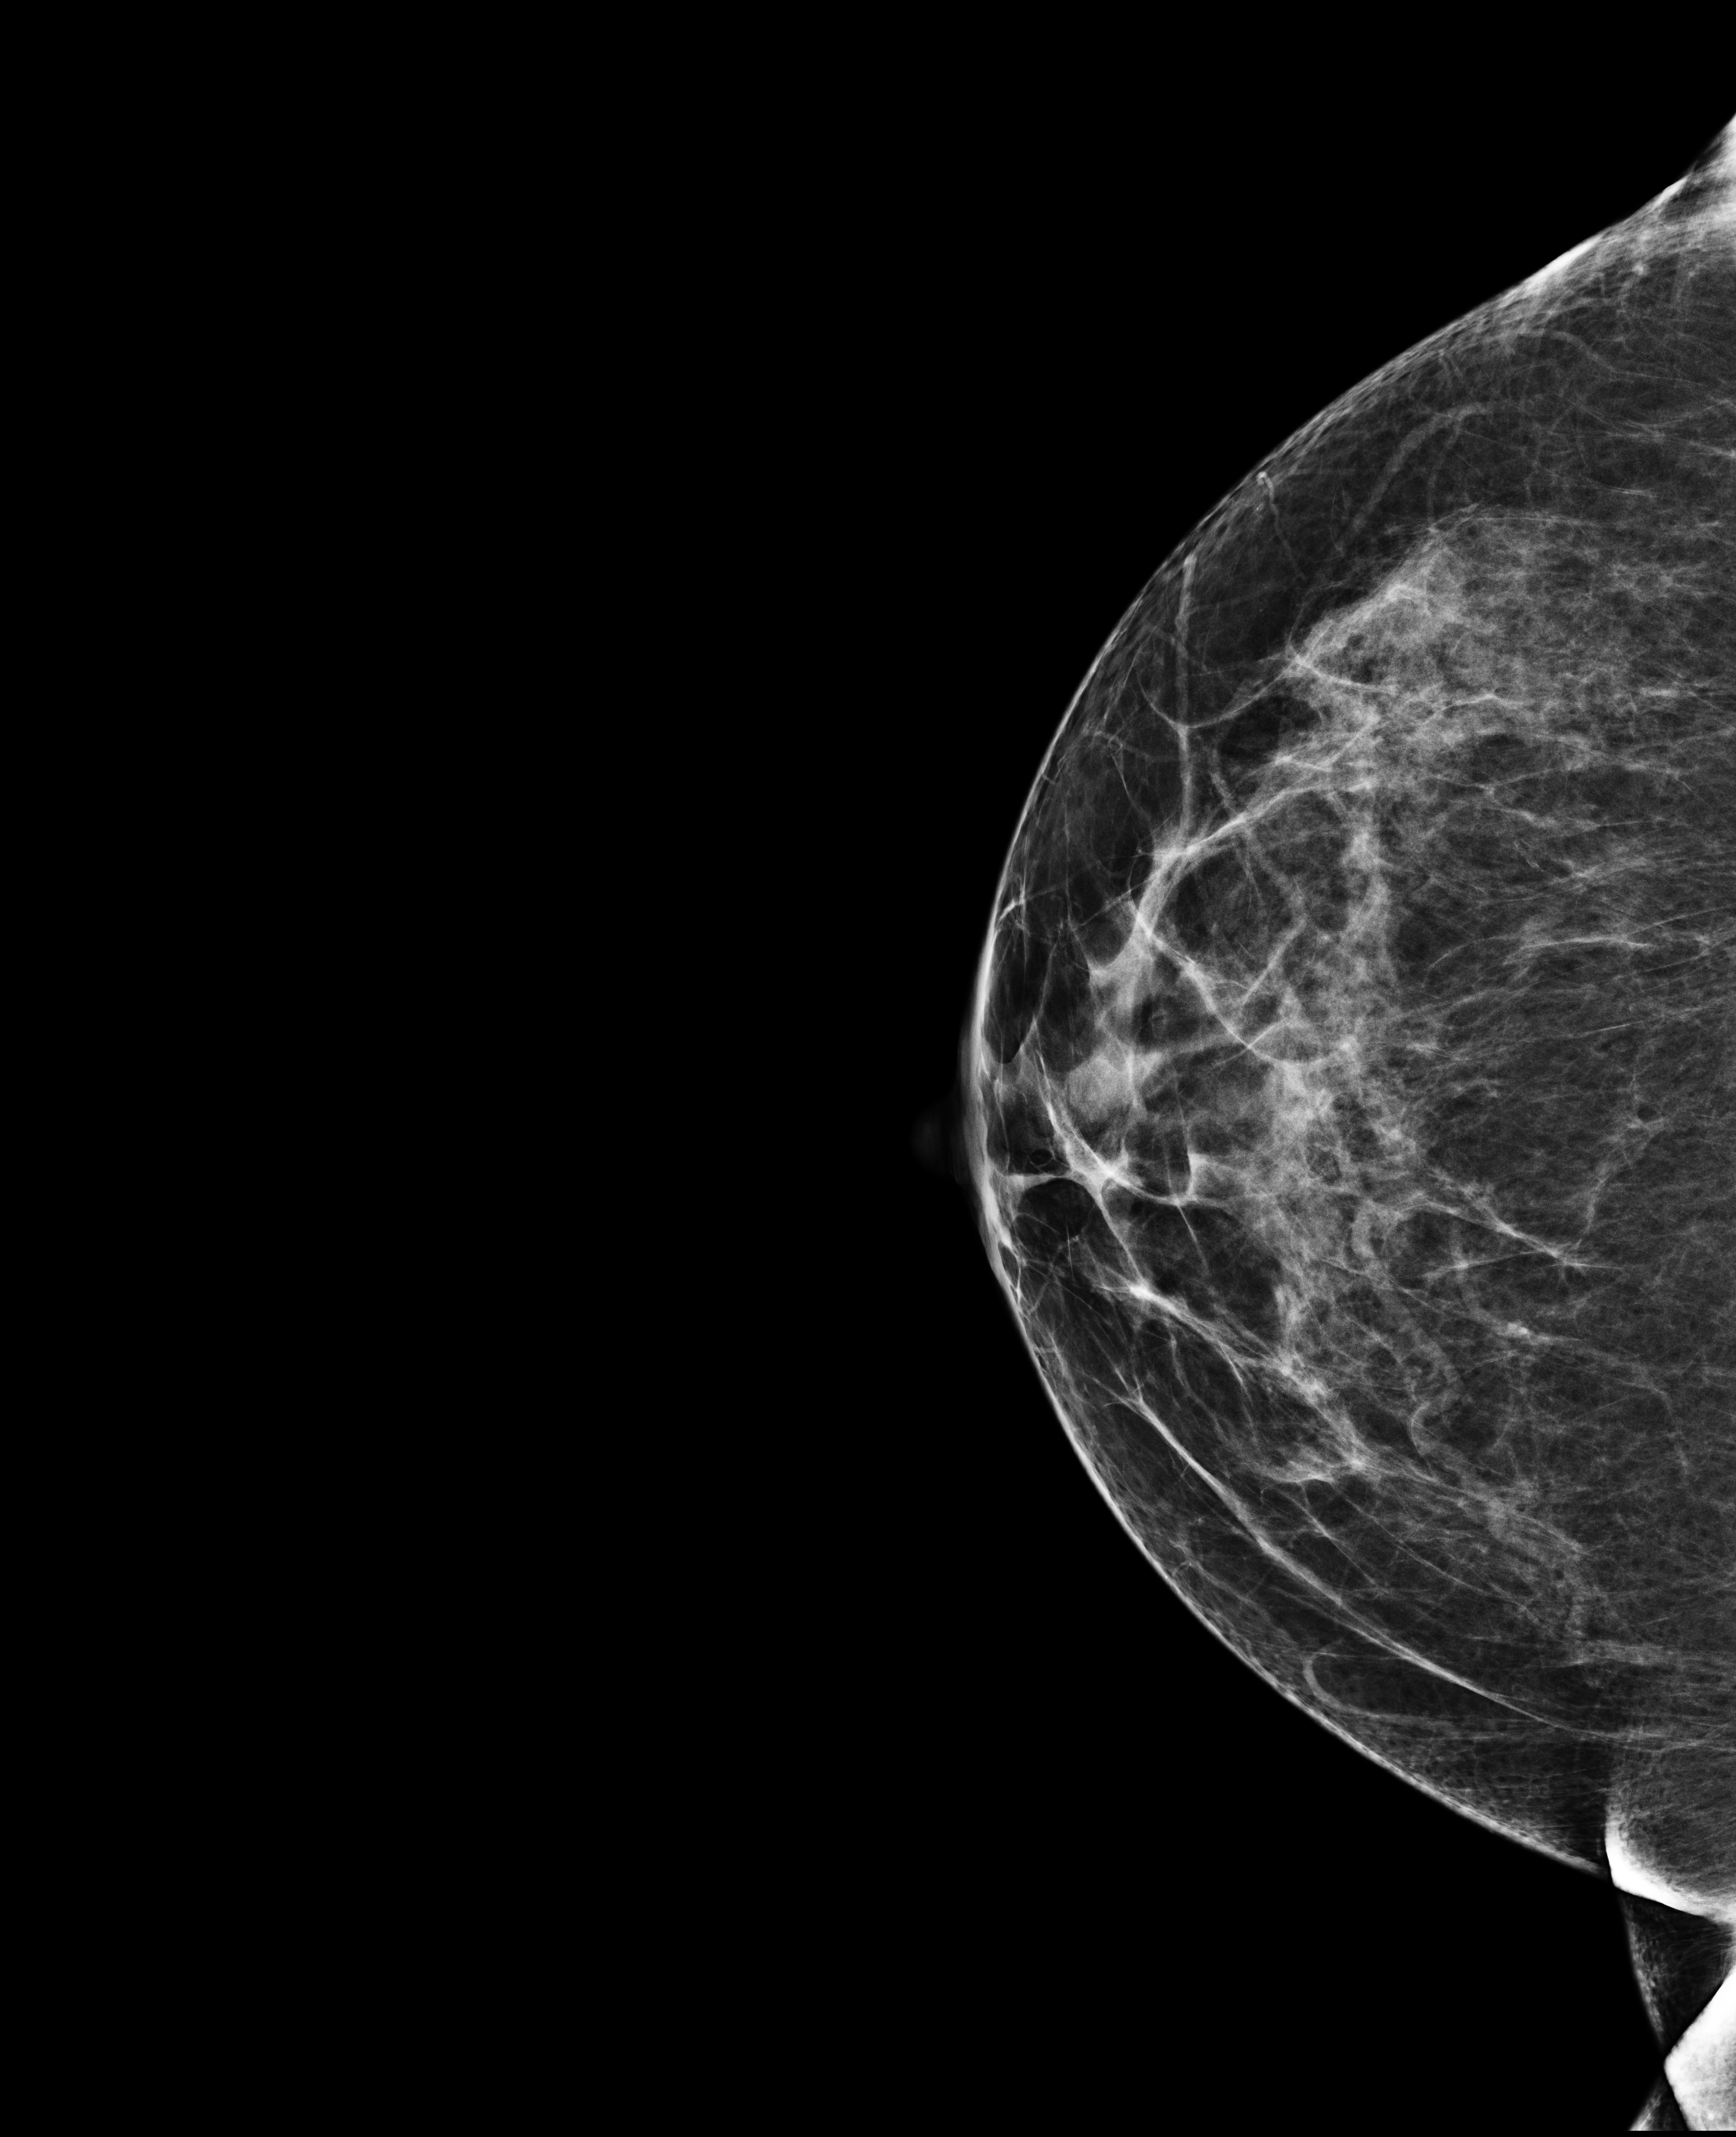
Digital mammogram (FFDM); right breast; craniocaudal (CC) view; annual screening mammography examination; compressed breast thickness 62 mm. Patient: female, 56 years.
- BI-RADS breast density category at the screening exam (both breasts, scale 1–4): 3
- final BI-RADS assessment for this screening round (tomosynthesis exam, both breasts): category 1
- recall: recalled for additional imaging after this screen